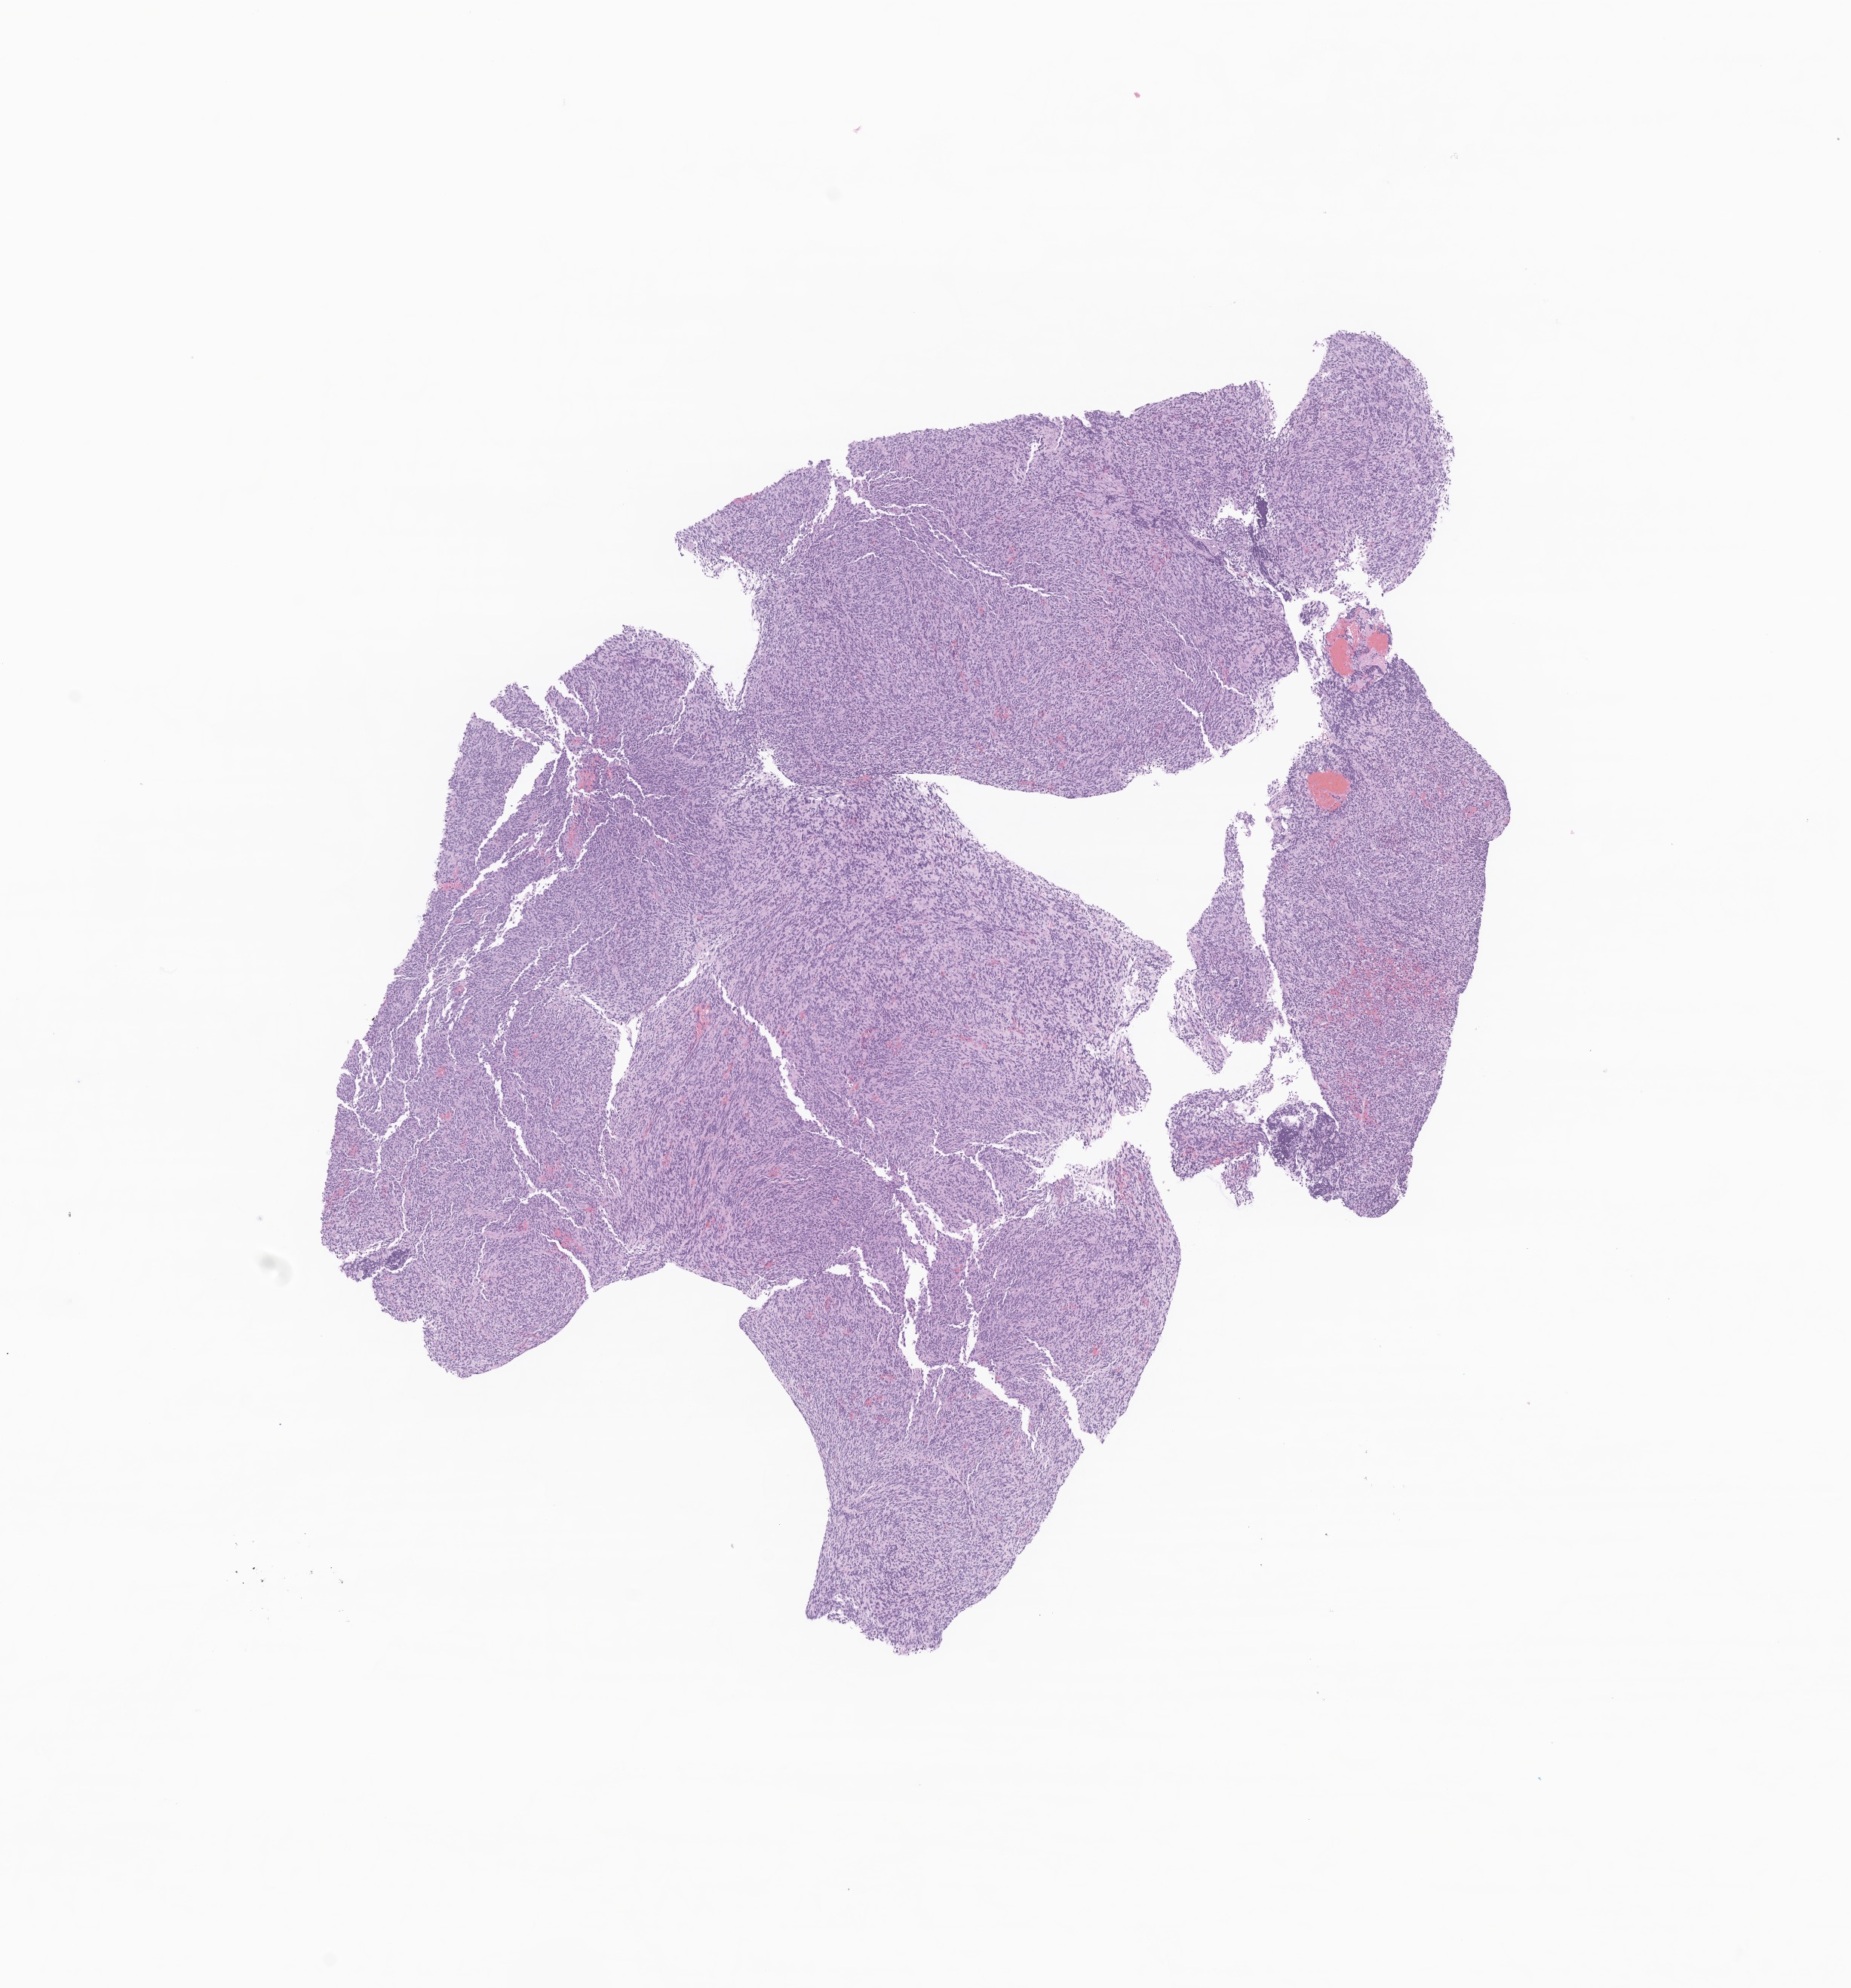
Digitized H&E-stained section of tumor tissue from the brain, a low-resolution overview of the entire scanned area, about 10.3 x 11.1 mm; FFPE section. Female patient, age 211 months.
• diagnosis: Glioma, malignant